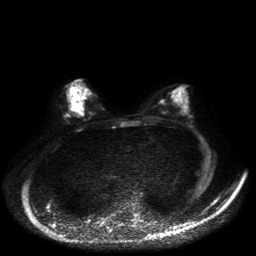
Breast MRI, one axial slice; diffusion-weighted series; image 2 of 4 stored at this slice position (different b-values; order by instance number); 1.5 T; 4 mm slice thickness; 256 × 256 image matrix, field of view 360 × 360 mm. Female patient.
Structures marked on this image (manually delineated by an expert):
- tumour on diffusion-weighted imaging: bounding box <75,103,78,107> (left, top, right, bottom; pixels)